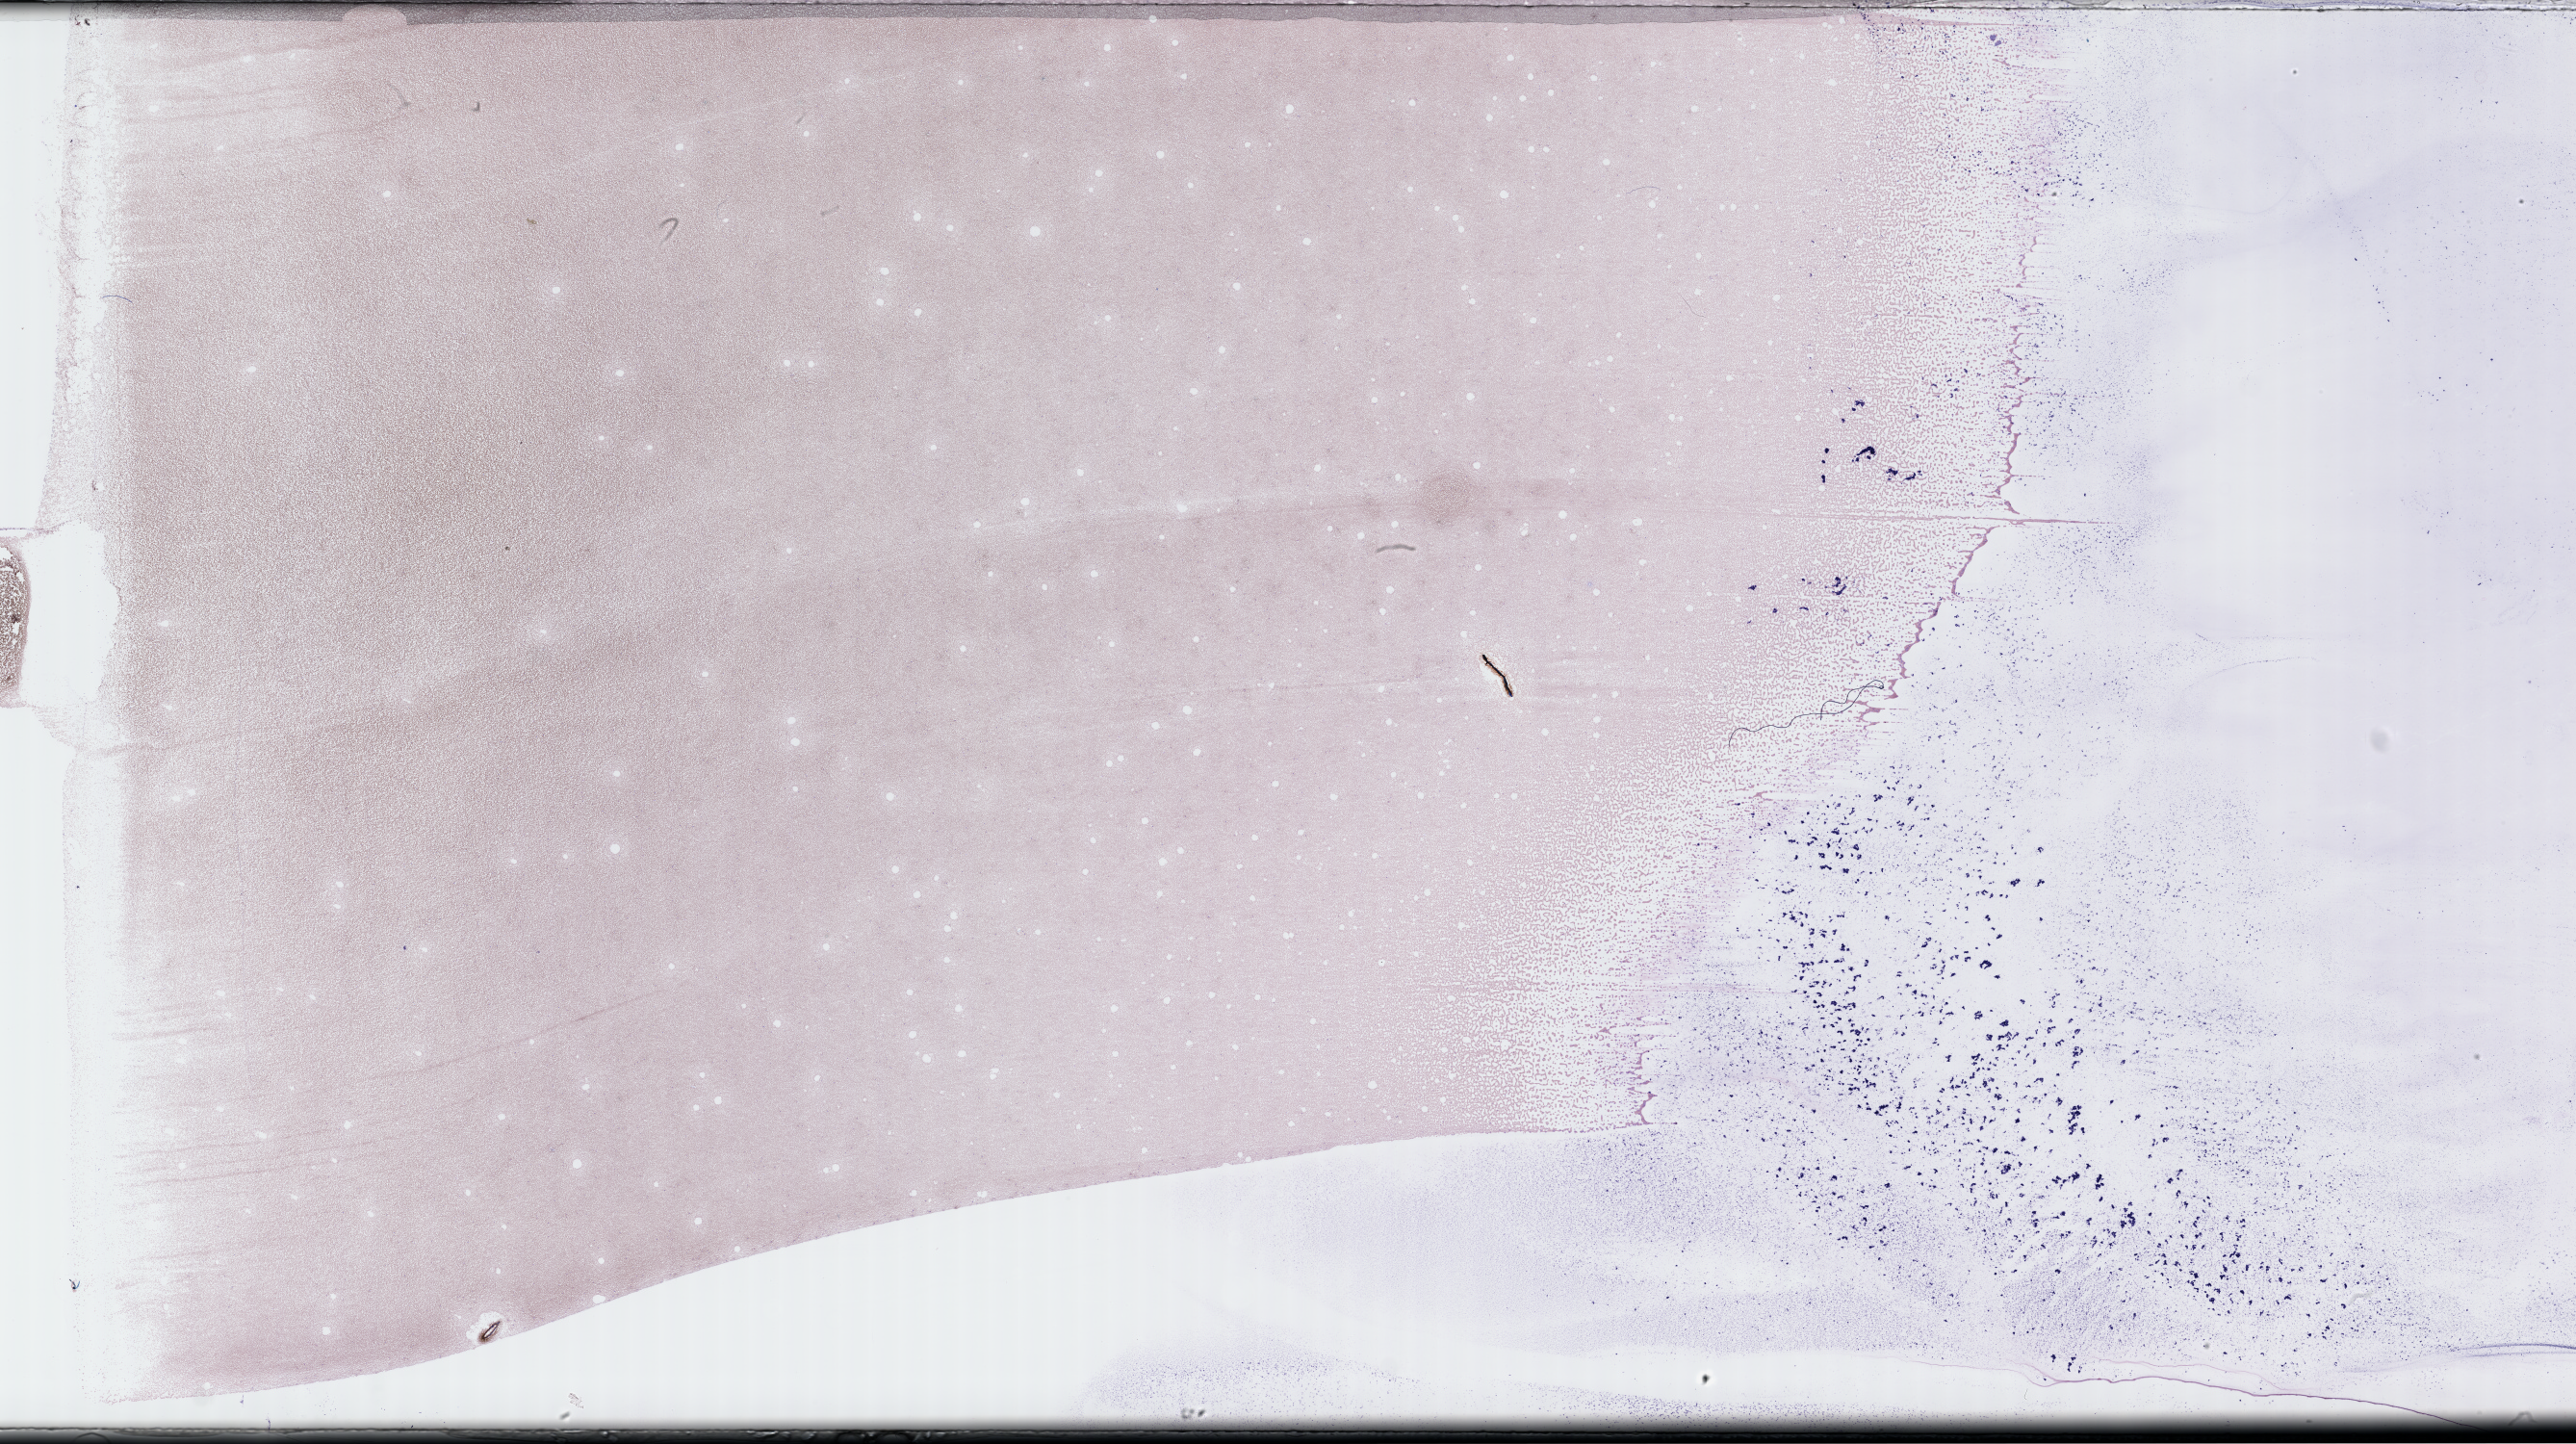
Whole-slide image of a whole blood smear, Wright–Giemsa stain — low-resolution overview of the scanned area, about 43.2 x 24.2 mm; specimen time point: collected on treatment. Patient sex: male.
From a patient with: Plasma Cell Myeloma.